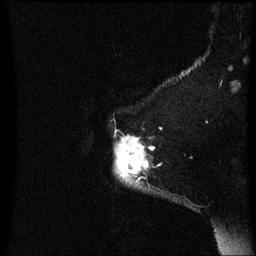
Breast MRI (dynamic contrast-enhanced), one sagittal slice. Slice 54 of 60 in the series (ordered by position). Dynamic contrast-enhanced series, image 2 of 3 at this slice position (ordered by acquisition). 1.5 T. TE 4.2 ms, TR 8.4 ms. 2 mm slice thickness. 256 × 256 image matrix. Female patient, age 54 years. From the clinical record (not read from this slice): setting: breast cancer imaged before/during neoadjuvant chemotherapy; receptor status: HR-positive, HER2-negative.
Structures marked on this image (semi-automatic segmentation, software-assisted and operator-edited):
- analysis volume of interest (the breast-tissue region the enhancement analysis was run in; not a lesion): bounding box <116,136,156,189> (left, top, right, bottom; pixels)
- tumour enhancement mask (voxels above the 70 % enhancement threshold inside the analysis volume of interest): <116,136,155,181>